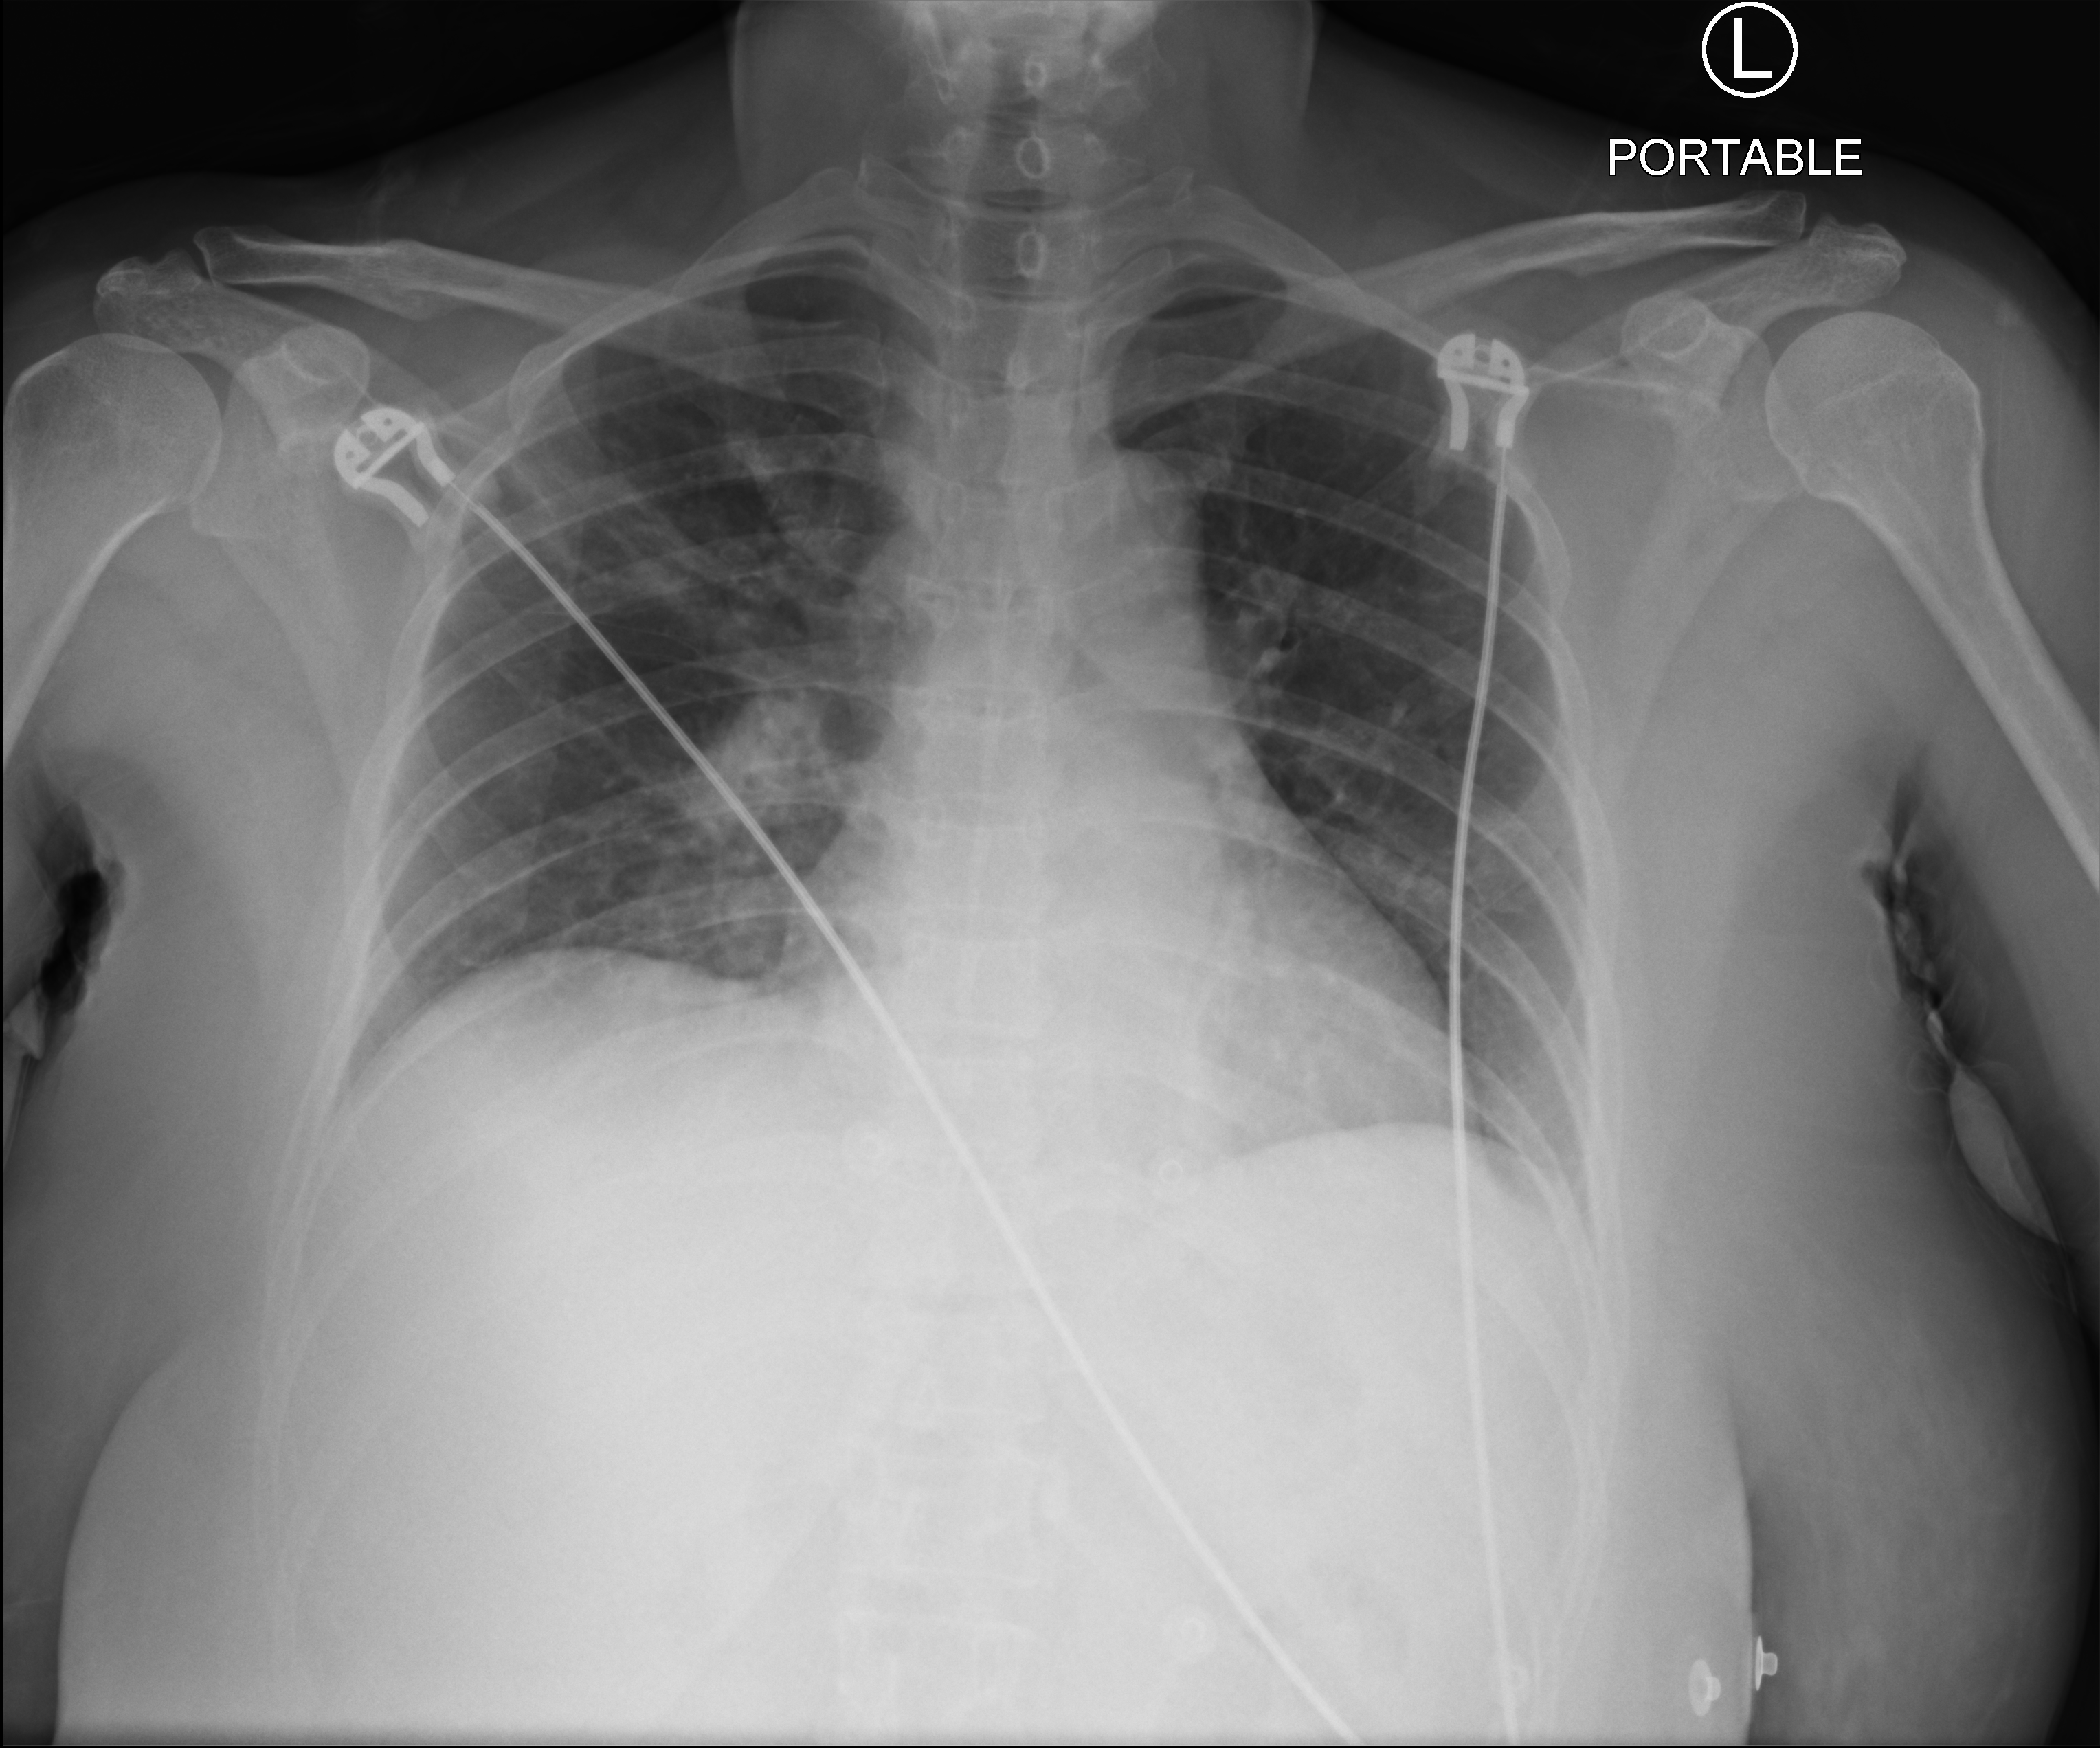
Chest X-ray (portable); anteroposterior (AP) projection. Patient hospitalised with COVID-19; male, aged 18–59 years.
From the hospital-stay record, not from the radiograph (when in the stay this image was taken is not recorded): admitted to intensive care during this hospital stay: no; mechanically ventilated during this hospital stay: no.